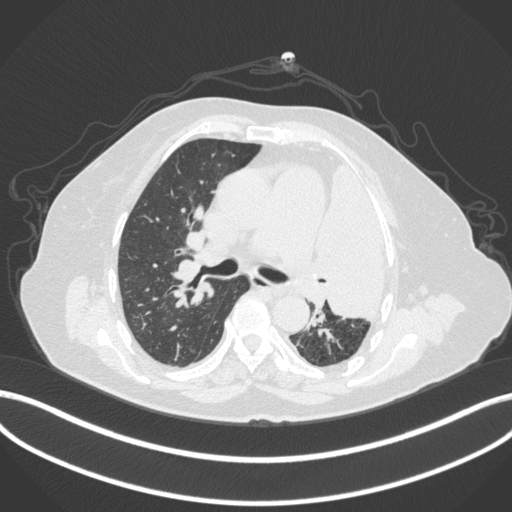
Chest CT, one axial slice; lung window (W 1500 / L -600 HU); 1 mm slice thickness; 512 × 512 image matrix. Patient: female, 75 years. Case-level facts recorded for this patient, not image findings: clinical TNM (as recorded): T3 N3 M1.
Outlined on this slice (bounding box drawn by a radiologist):
- lung tumour (recorded histology: adenocarcinoma): box from (x=313, y=154) to (x=396, y=327) px